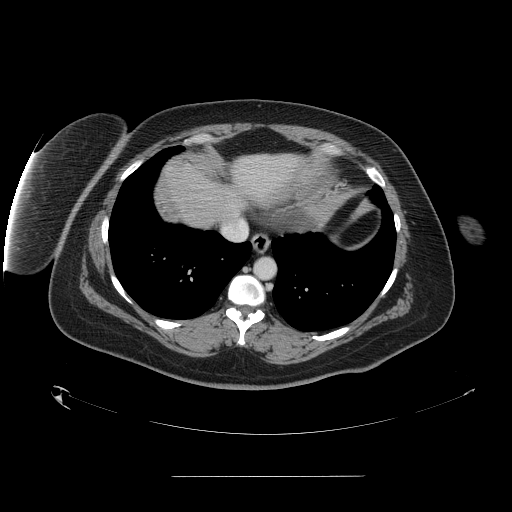
Contrast-enhanced abdominal CT, one axial slice. Slice 141 of 164 in the series (ordered by position). 120 kVp. Soft-tissue window (W 400 / L 40 HU). 2.5 mm slice thickness. 512 × 512 image matrix, field of view 495 × 495 mm. Female patient, age 52 years. From the clinical record (not read from this slice): diagnosis: colorectal cancer liver metastases, imaged before liver resection; multiple liver metastases: yes; largest metastasis: 3.5 cm; disease in both lobes: no.
Structures marked on this image (manually delineated by an expert):
- hepatic veins: bounding box [x1, y1, x2, y2] px = [223, 227, 227, 230]
- liver: [164, 157, 297, 228]
- planned liver remnant (the part of the liver to remain after resection): [185, 157, 290, 221]